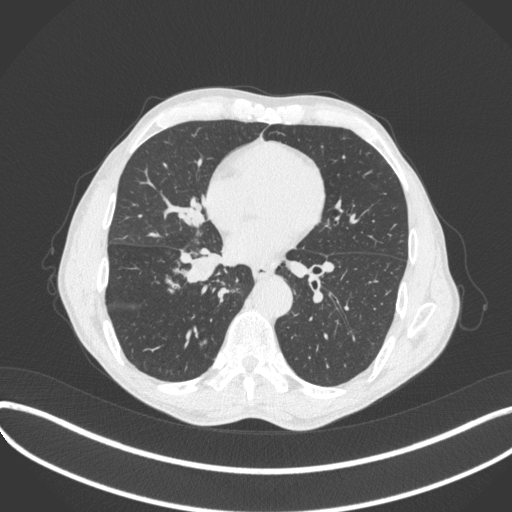
Chest CT, one axial slice. Position 191 of 481 along the scan axis. 120 kVp. Lung window (W 1500 / L -600 HU). 1 mm slice thickness. 512 × 512 image matrix, field of view 400 × 400 mm. Male patient, age 65 years. Case-level facts recorded for this patient, not image findings: clinical TNM (as recorded): T2a N0 M0.
Structures marked on this image (rectangle marked by the reading radiologist):
- lung tumour (recorded histology: squamous cell carcinoma): box from (x=178, y=245) to (x=226, y=285) px